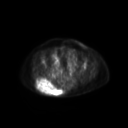
FDG PET of an extremity soft-tissue mass (from a PET/CT study), one axial slice; slice 66 of 267 in the series (ordered by position); 3.27 mm slice thickness; 128 × 128 image matrix, field of view 600 × 600 mm. Patient: female, 60 years. From the clinical record (not read from this slice): histological type: spindle cell suggestive of myxofibrosarcoma; grade: intermediate; site of the primary tumour: right buttock.
Structures marked on this image (expert contour drawn on MRI and transferred to this co-registered scan by the dataset authors):
- gross tumour volume (mass): bounding box <36,78,63,96> (left, top, right, bottom; pixels)